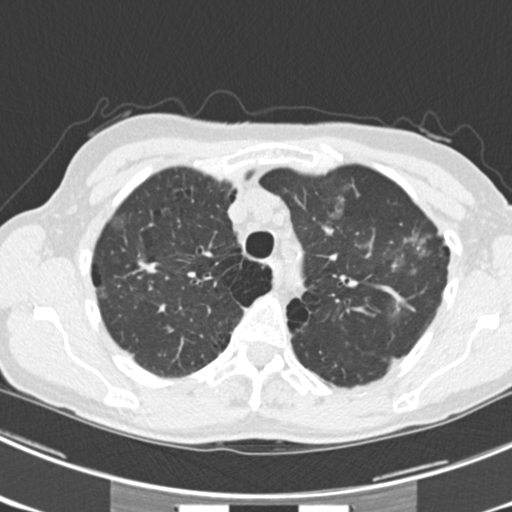
Chest CT (low-dose screening protocol), one axial image. Third annual screen. Lung window (W 1500 / L -600 HU). 2 mm slice thickness. 120 kVp. Slice 53 of 225 in the series. 512 × 512 image matrix. Female participant, aged 63 years at enrolment.
Expert-annotated lung lesion, bounding box (x1, y1, x2, y2) in pixels: (379, 218, 453, 278). The screening reader recorded 9 non-calcified nodules or masses ≥4 mm on this exam; which of them this box marks is not recorded. Lung cancer was diagnosed 15 days after this screen: bronchiolo-alveolar adenocarcinoma, NOS, right upper lobe, right middle lobe, right lower lobe, left upper lobe, left lower lobe, moderately differentiated (G2), stage IV (AJCC 6th edition).